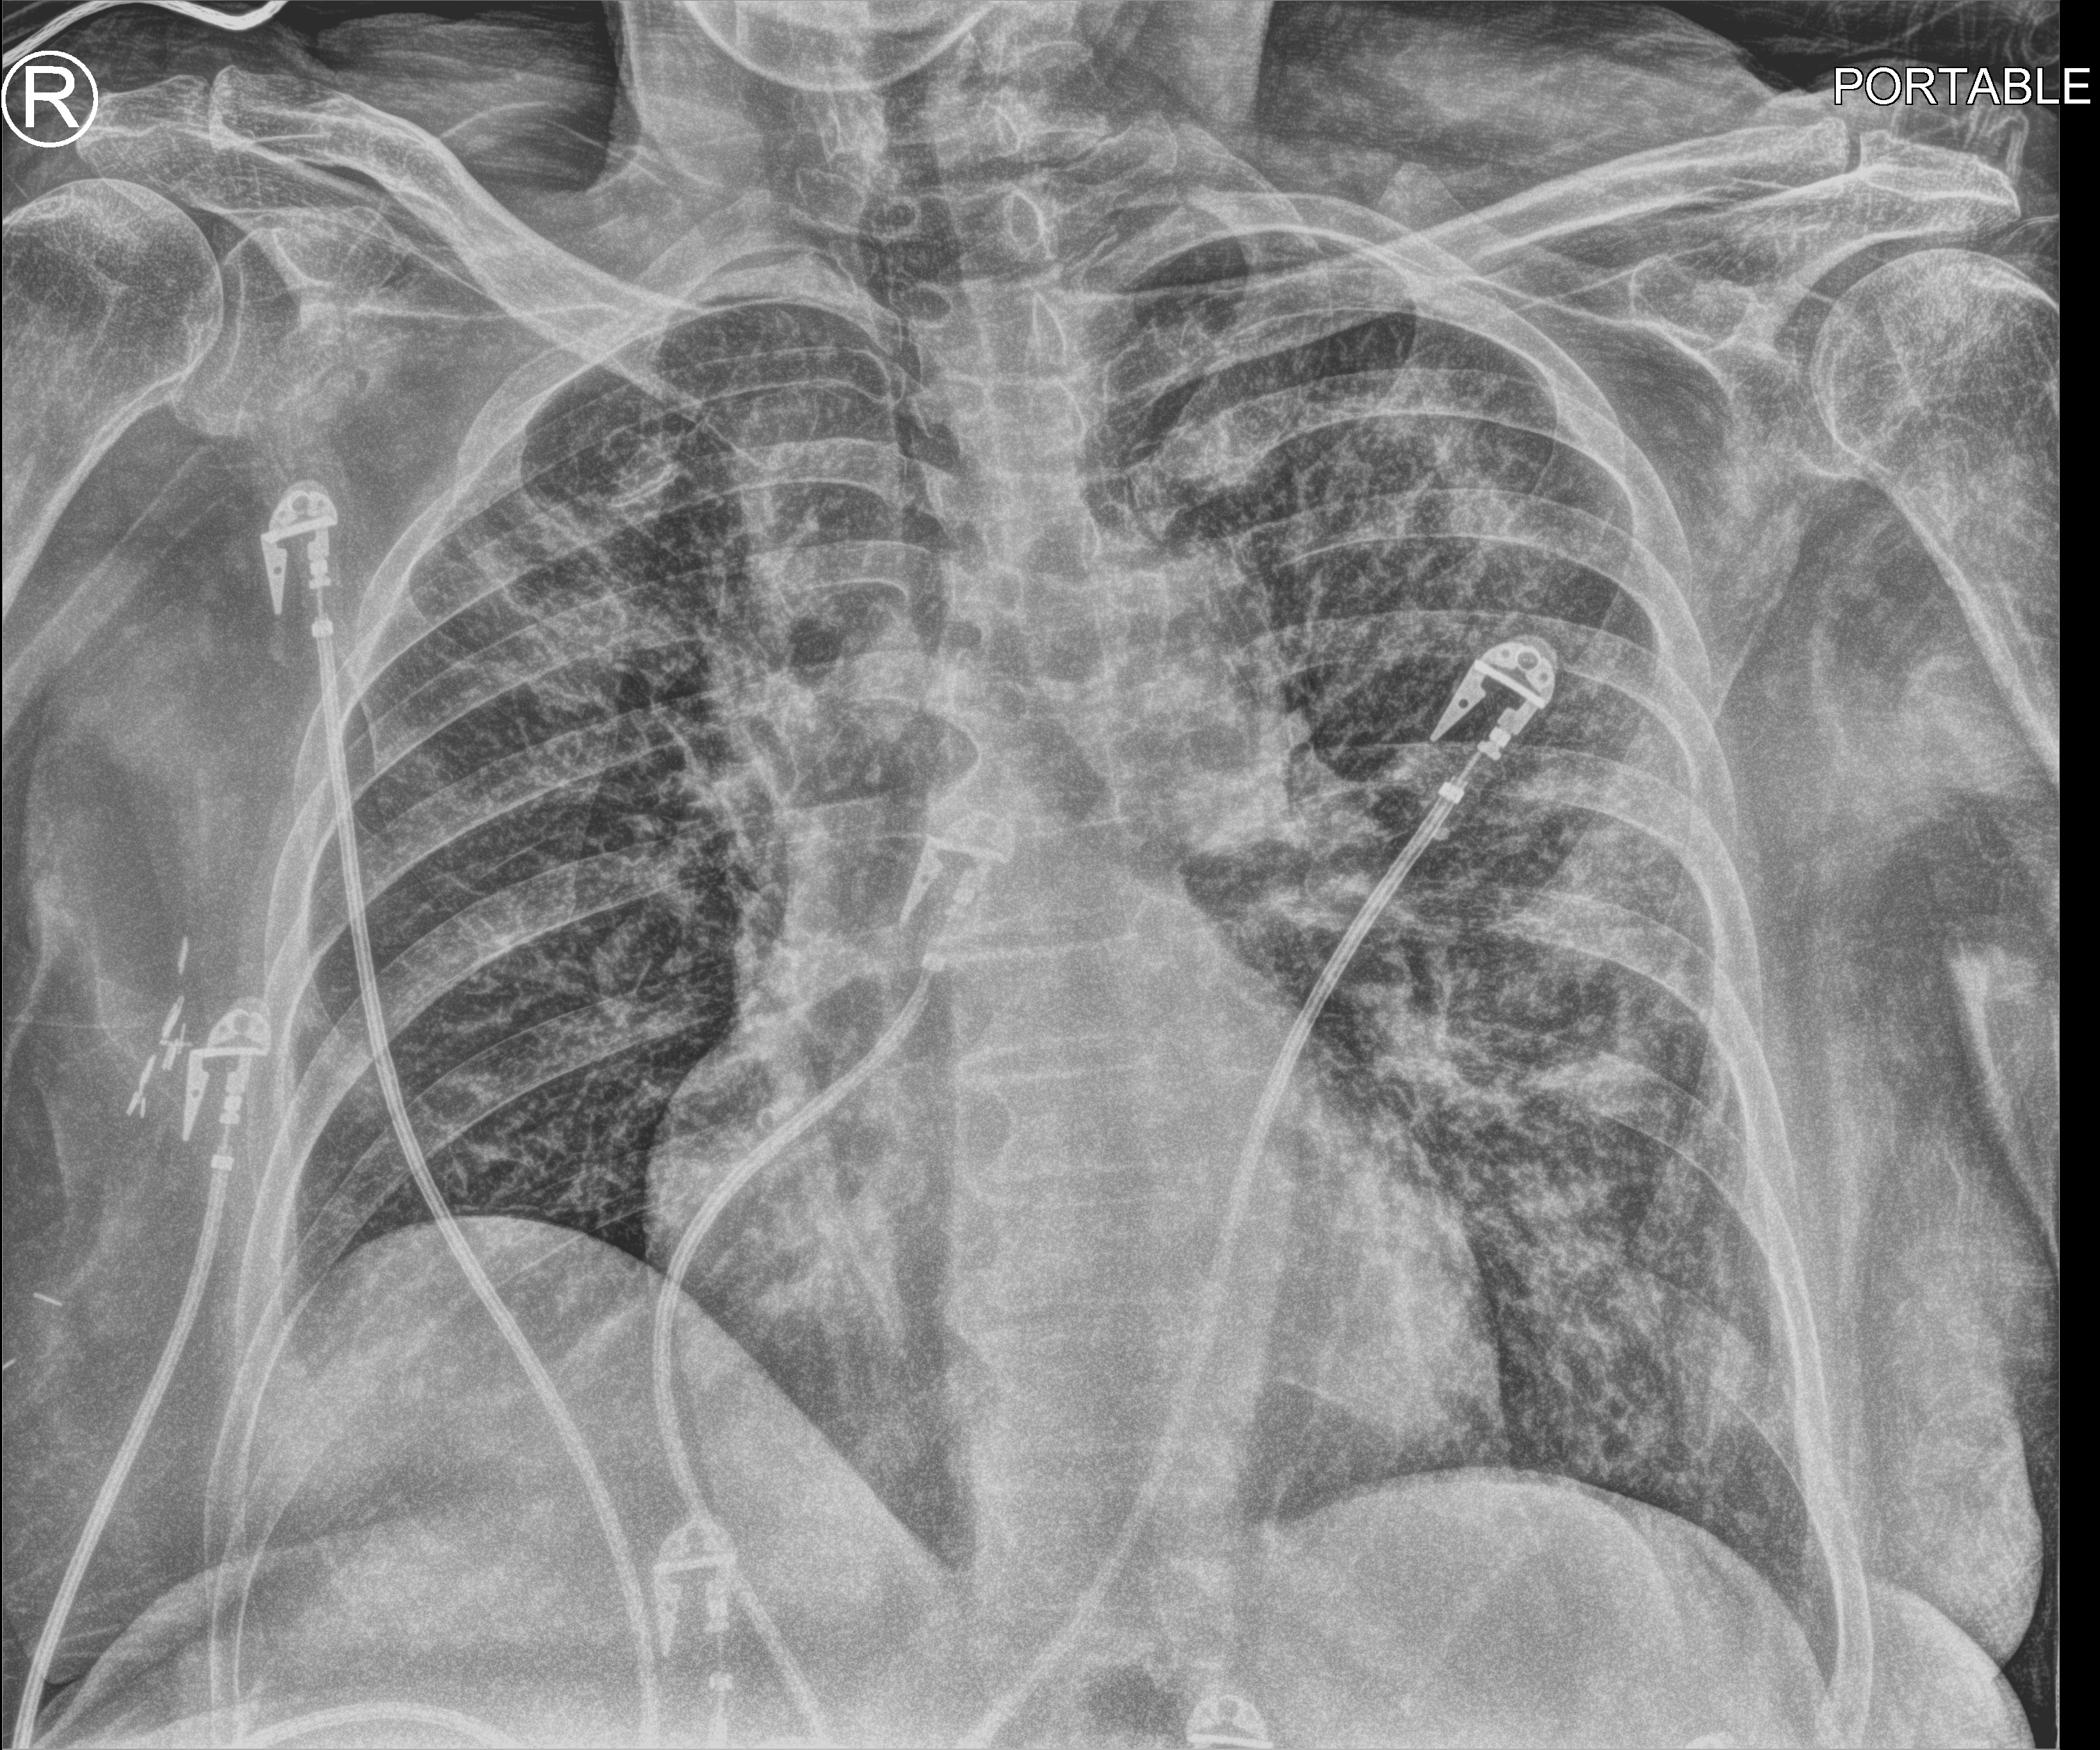
Bedside chest radiograph (computed radiography), anteroposterior (AP) projection. Female patient hospitalised with COVID-19, age 60–74 years.
Hospital-stay facts (about this admission, not read from this image; timing relative to this image not recorded): mechanically ventilated during this hospital stay: no.